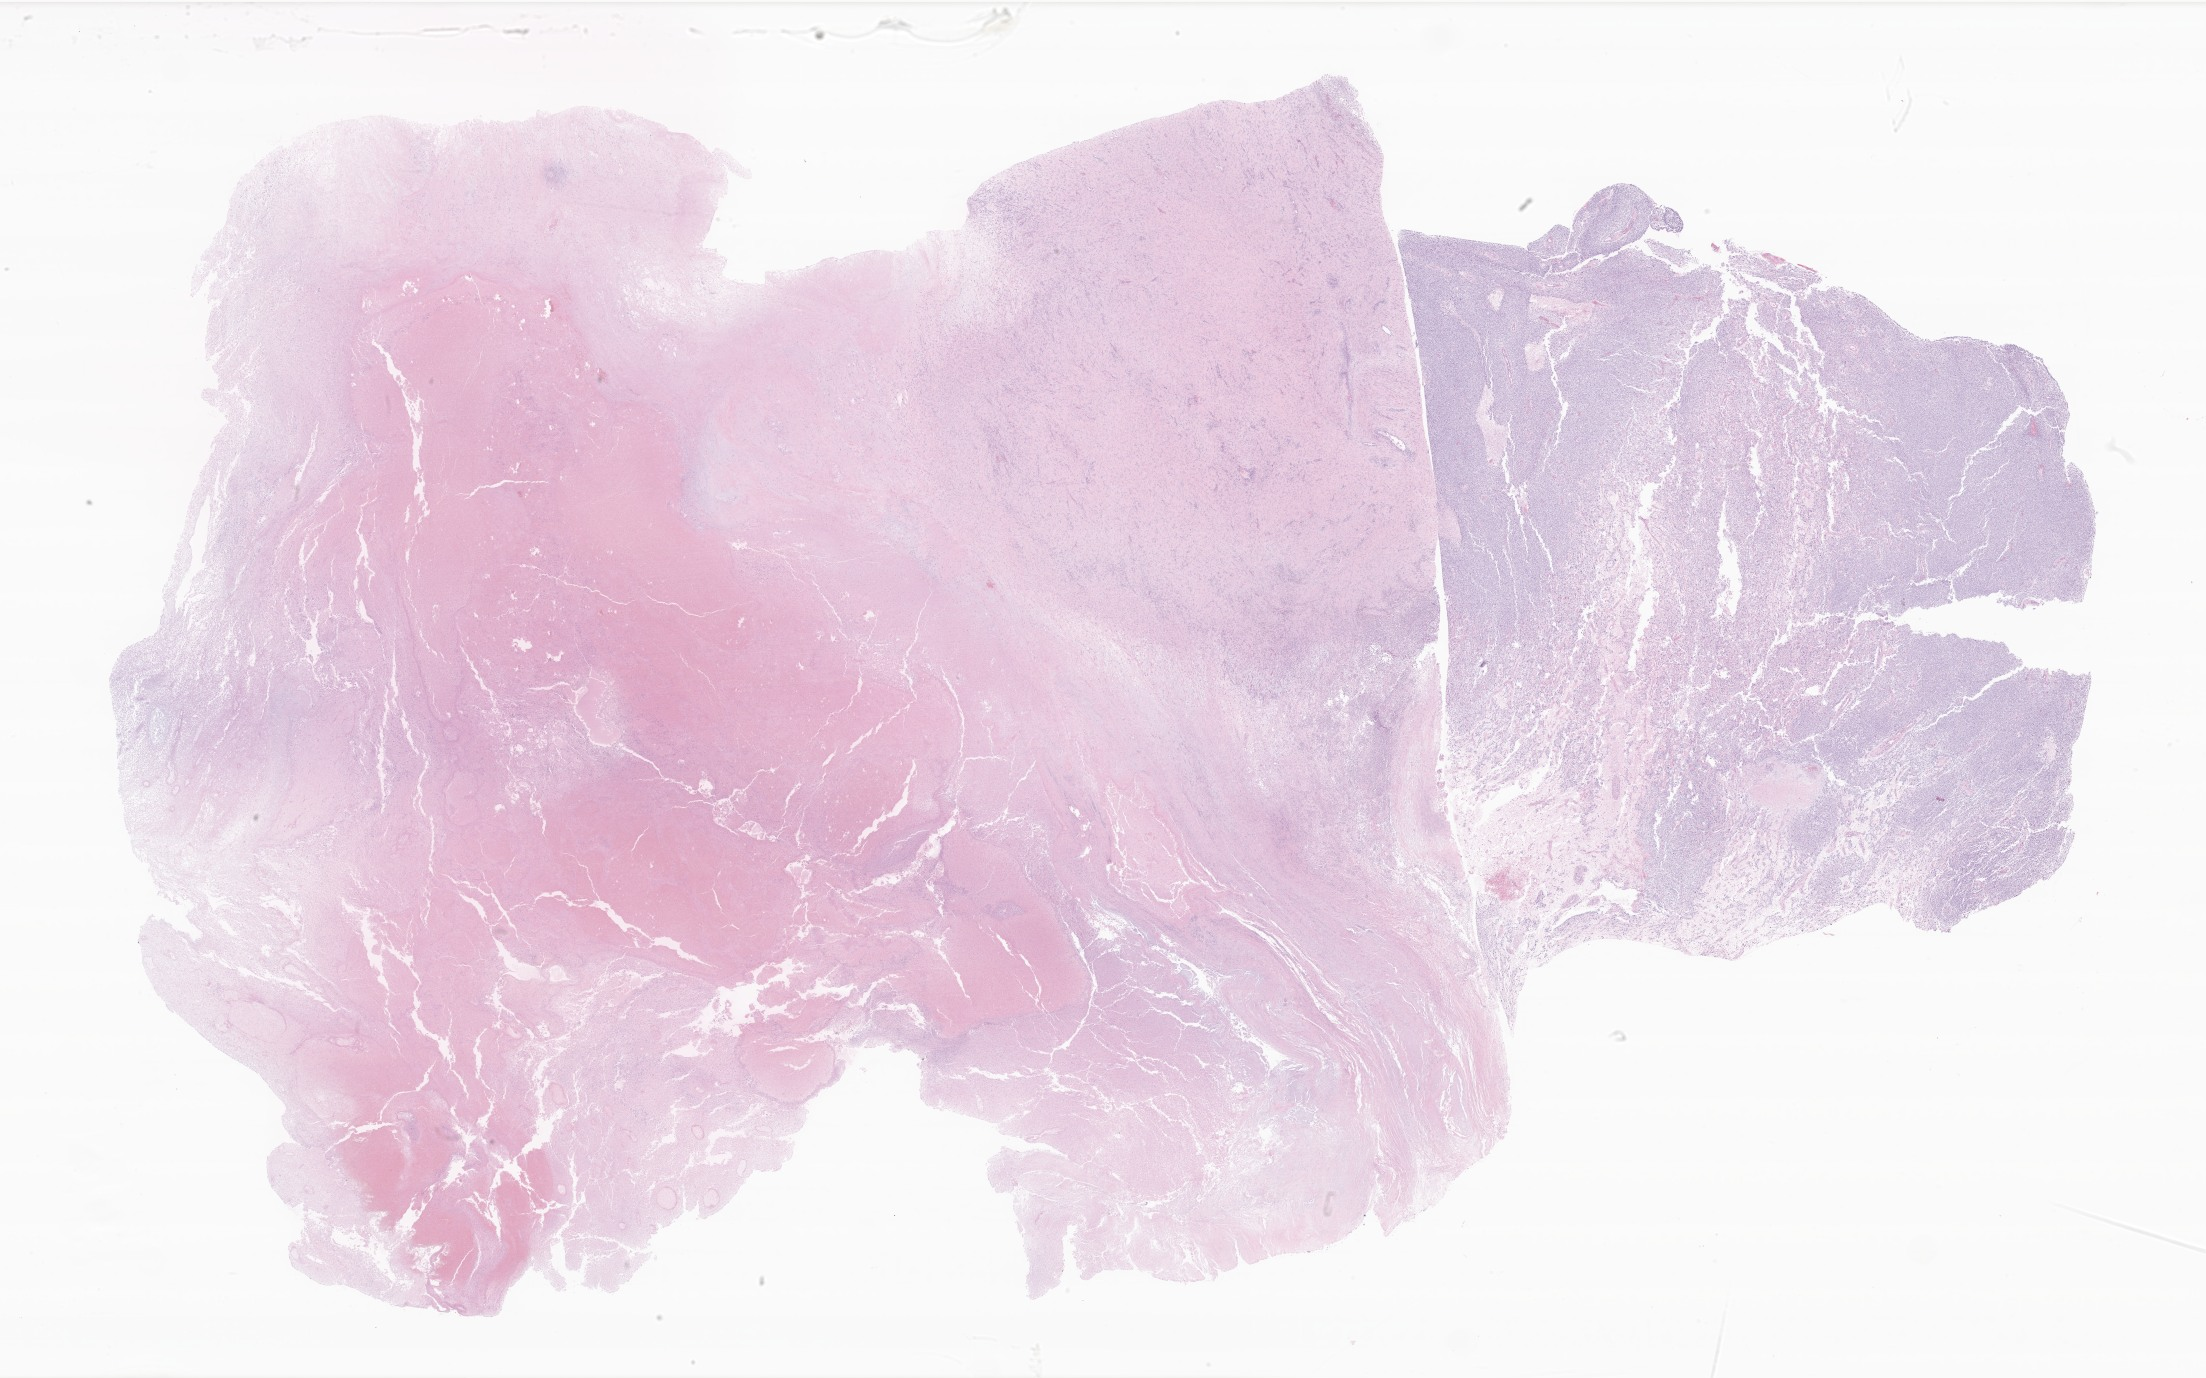
Digitized hematoxylin and eosin (H&E)-stained section of tumor tissue from the soft tissue of upper extremity — whole scanned area (about 37.2 x 23.2 mm) shown as a low-resolution overview, formalin-fixed, paraffin-embedded (FFPE) tissue. Patient: male, age 173 months (14 years 5 months).
Diagnosis: Sarcoma, NOS.